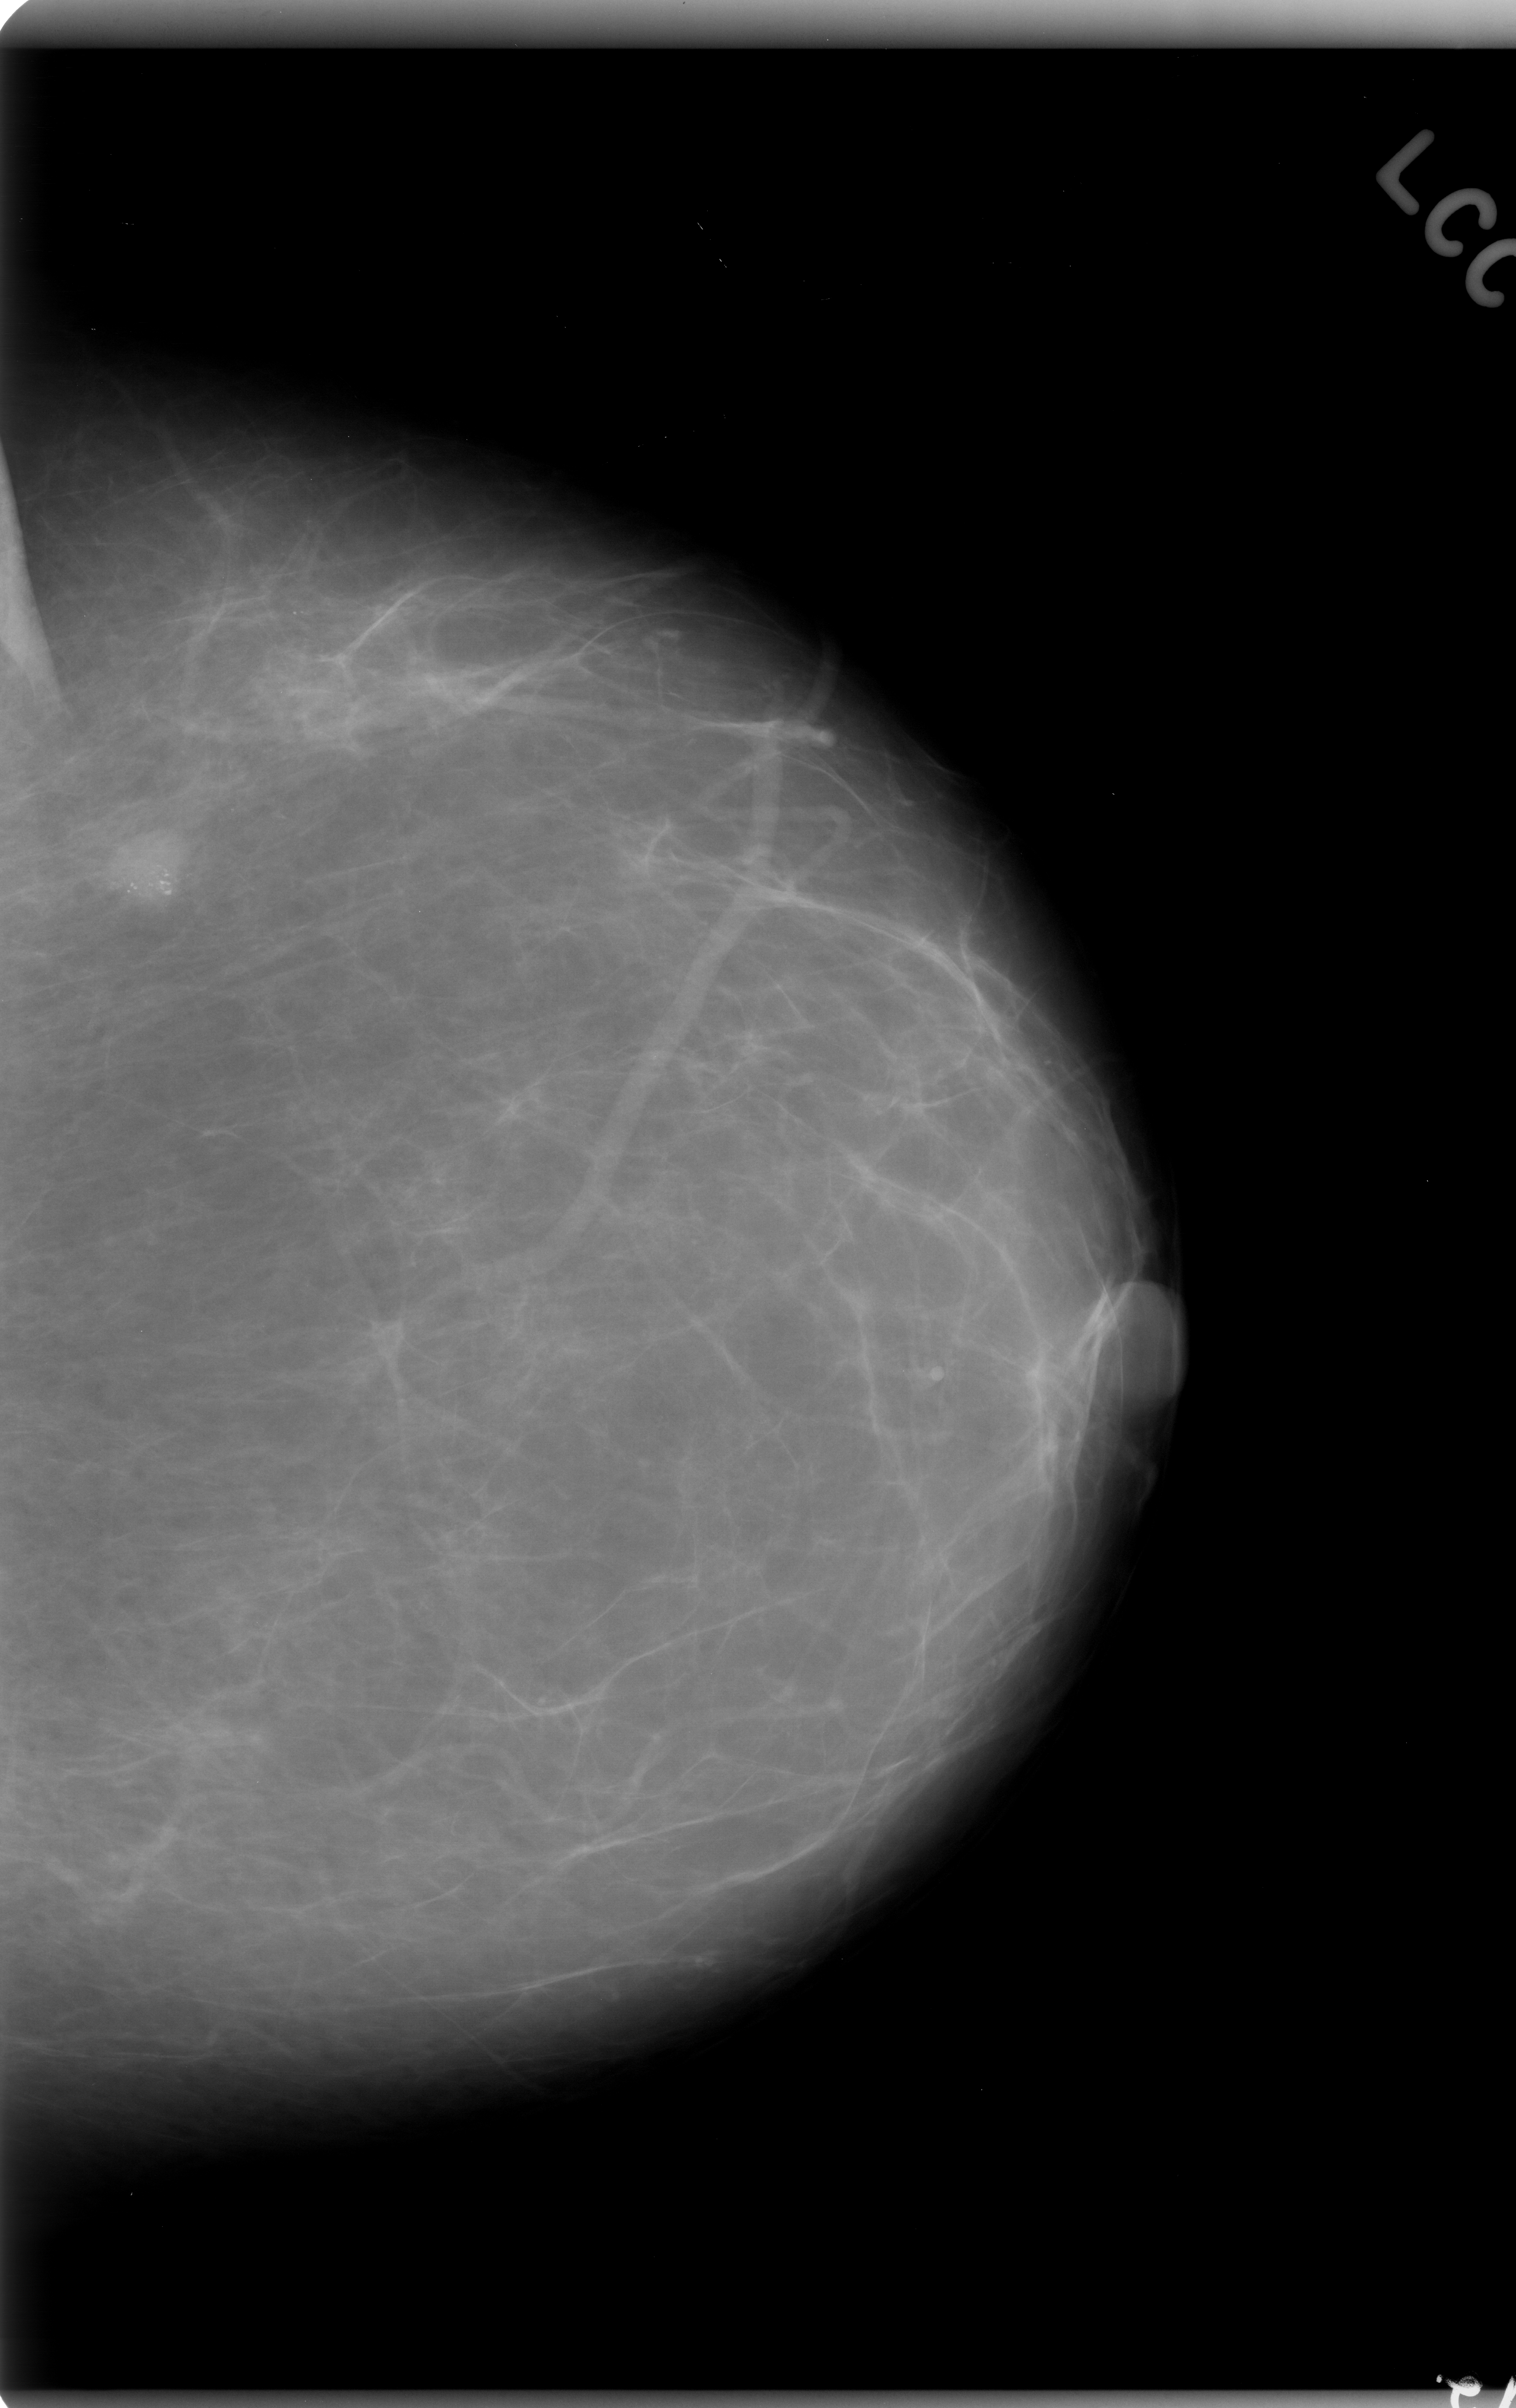
Scanned film-screen mammogram; left breast; craniocaudal (CC) view; BI-RADS breast density category 1 (scale 1–4); 1516 × 2408 image matrix.
Expert-marked regions of interest on this film, with their recorded descriptors:
- calcifications, morphology pleomorphic, distribution clustered; BI-RADS assessment category 4; pathology (as recorded): malignant: bounding box <71,582,463,954> (left, top, right, bottom; pixels)